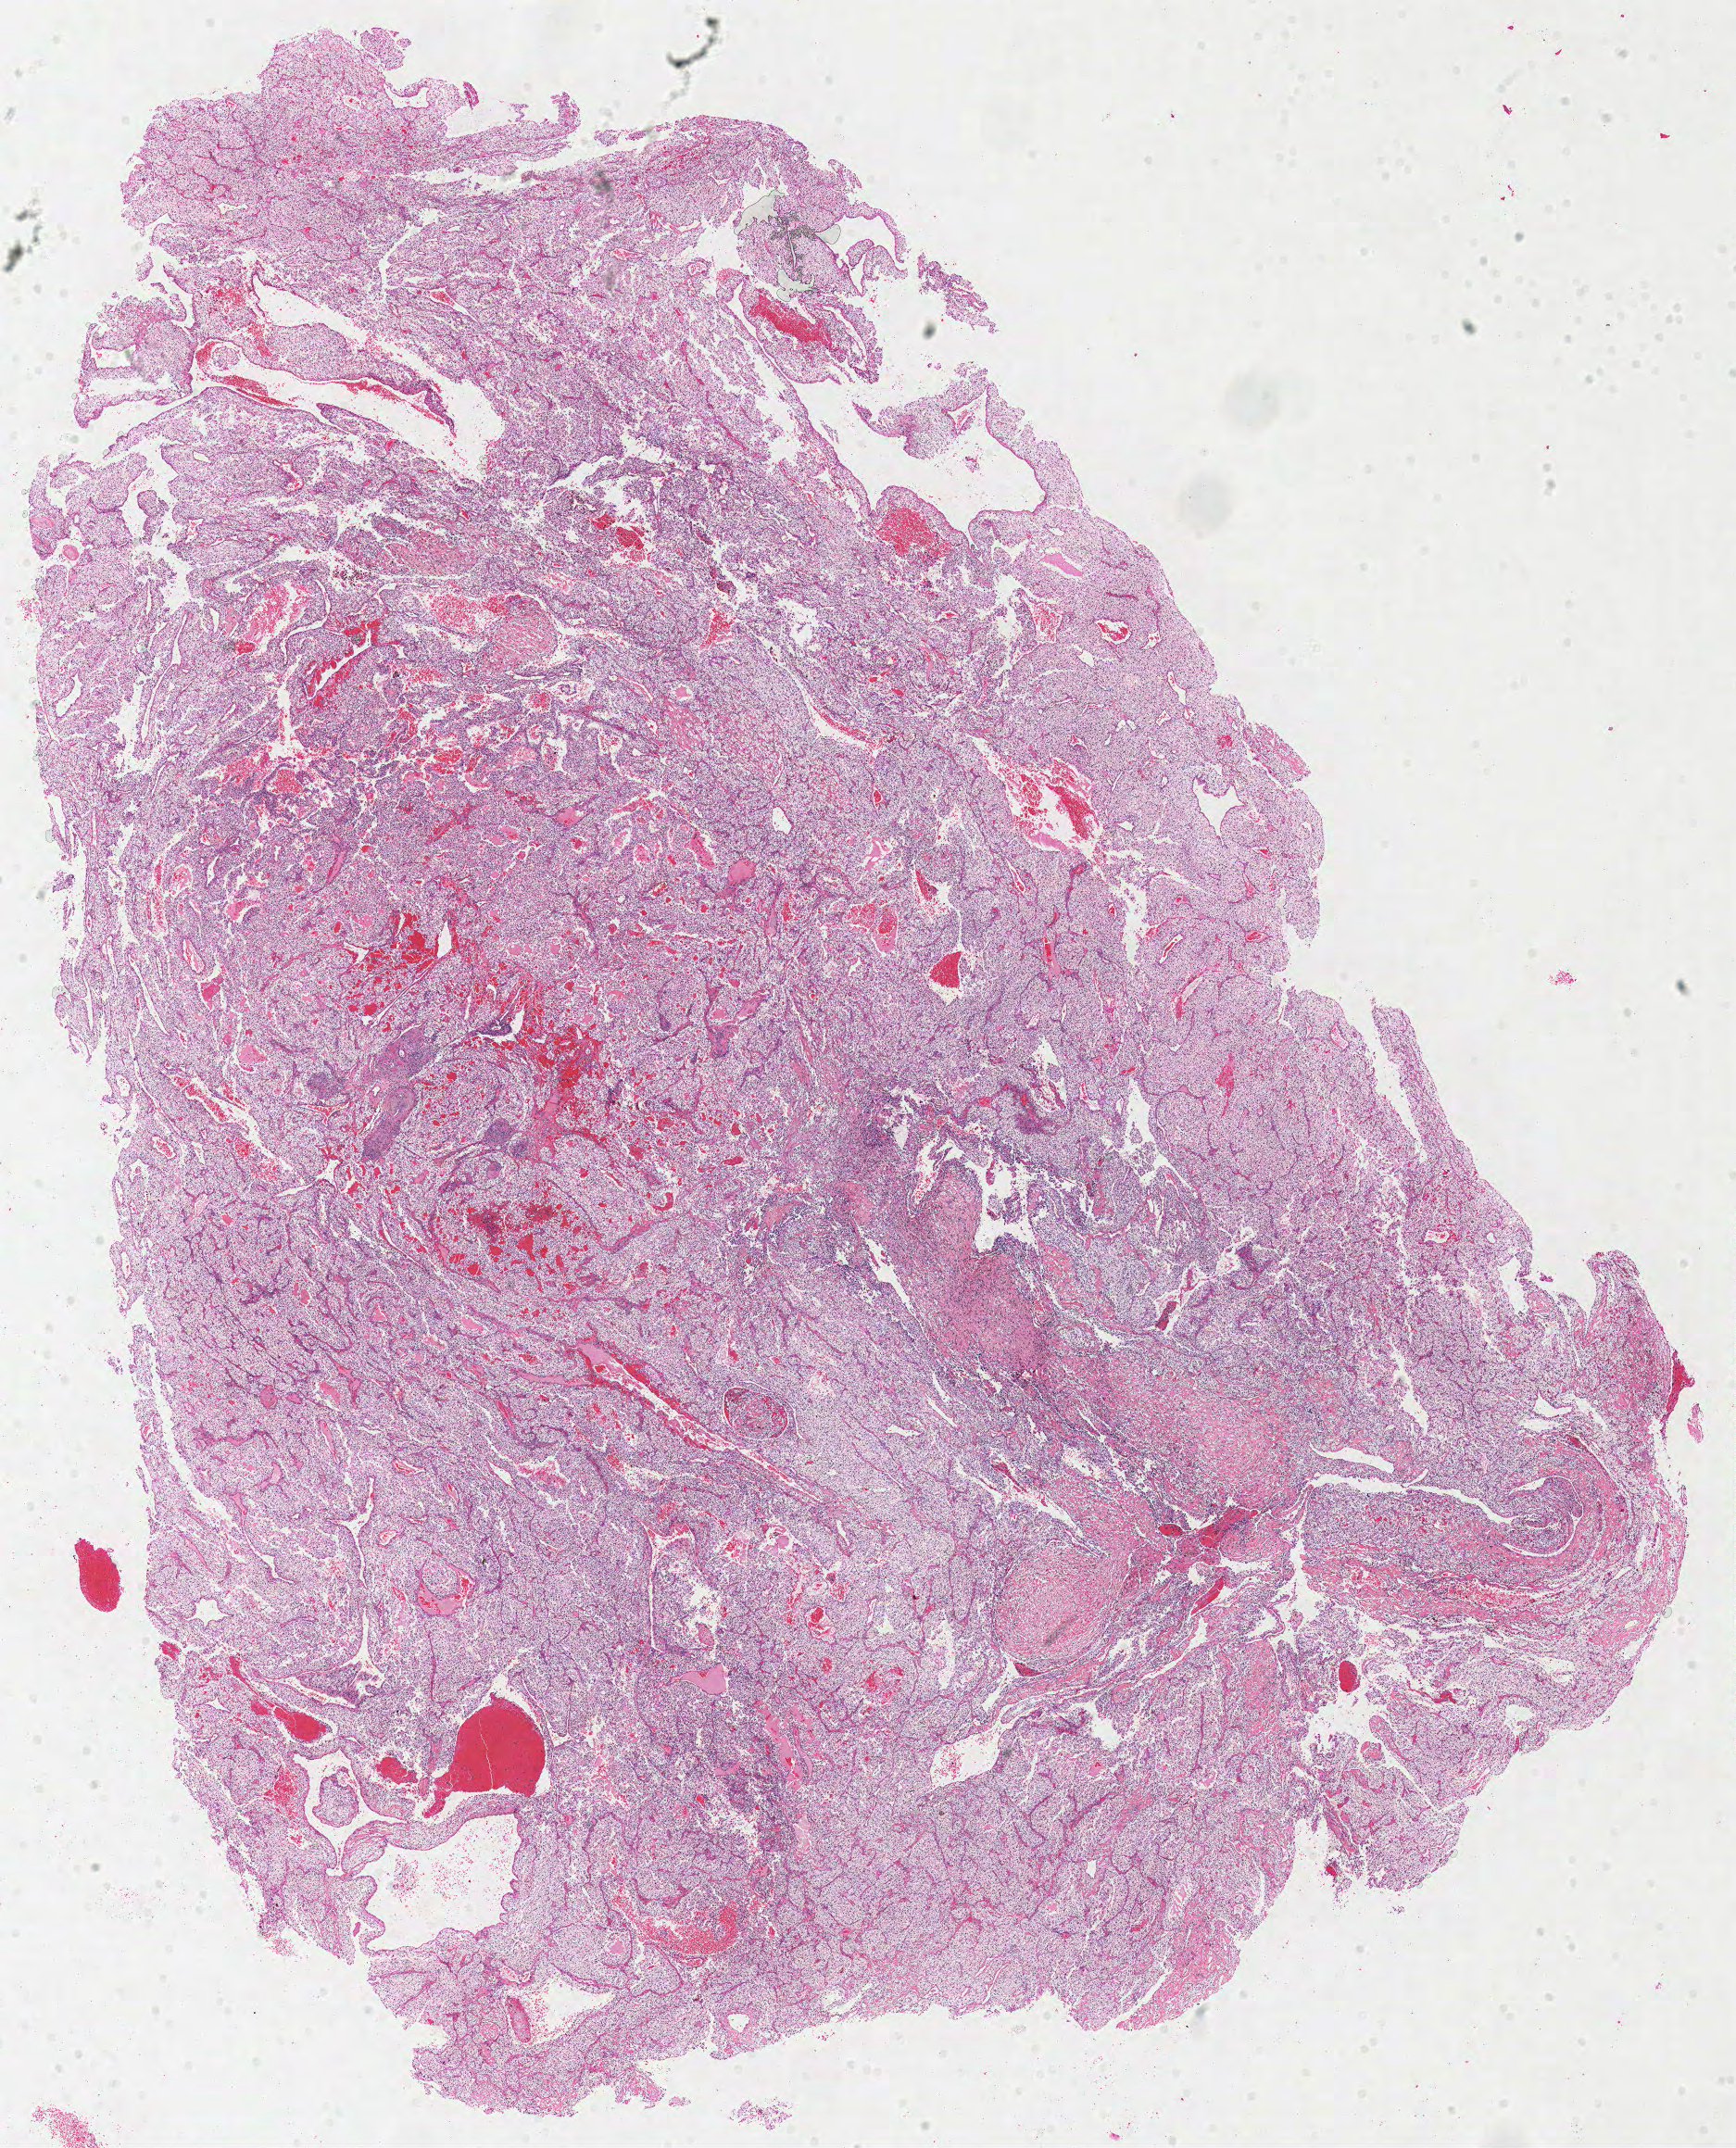
H&E whole-slide image, whole scanned area (about 14.8 x 18.3 mm) shown as a low-resolution overview. Formalin-fixed paraffin-embedded (FFPE) diagnostic section. Kidney, primary tumour sample. Female patient; age at initial diagnosis 70 years. Histologic grade: G2 (moderately differentiated).
AJCC pathologic stage: III. Pathologic diagnosis: Clear cell adenocarcinoma, NOS. Lymph nodes positive (case pathology): 0 of 2 examined.